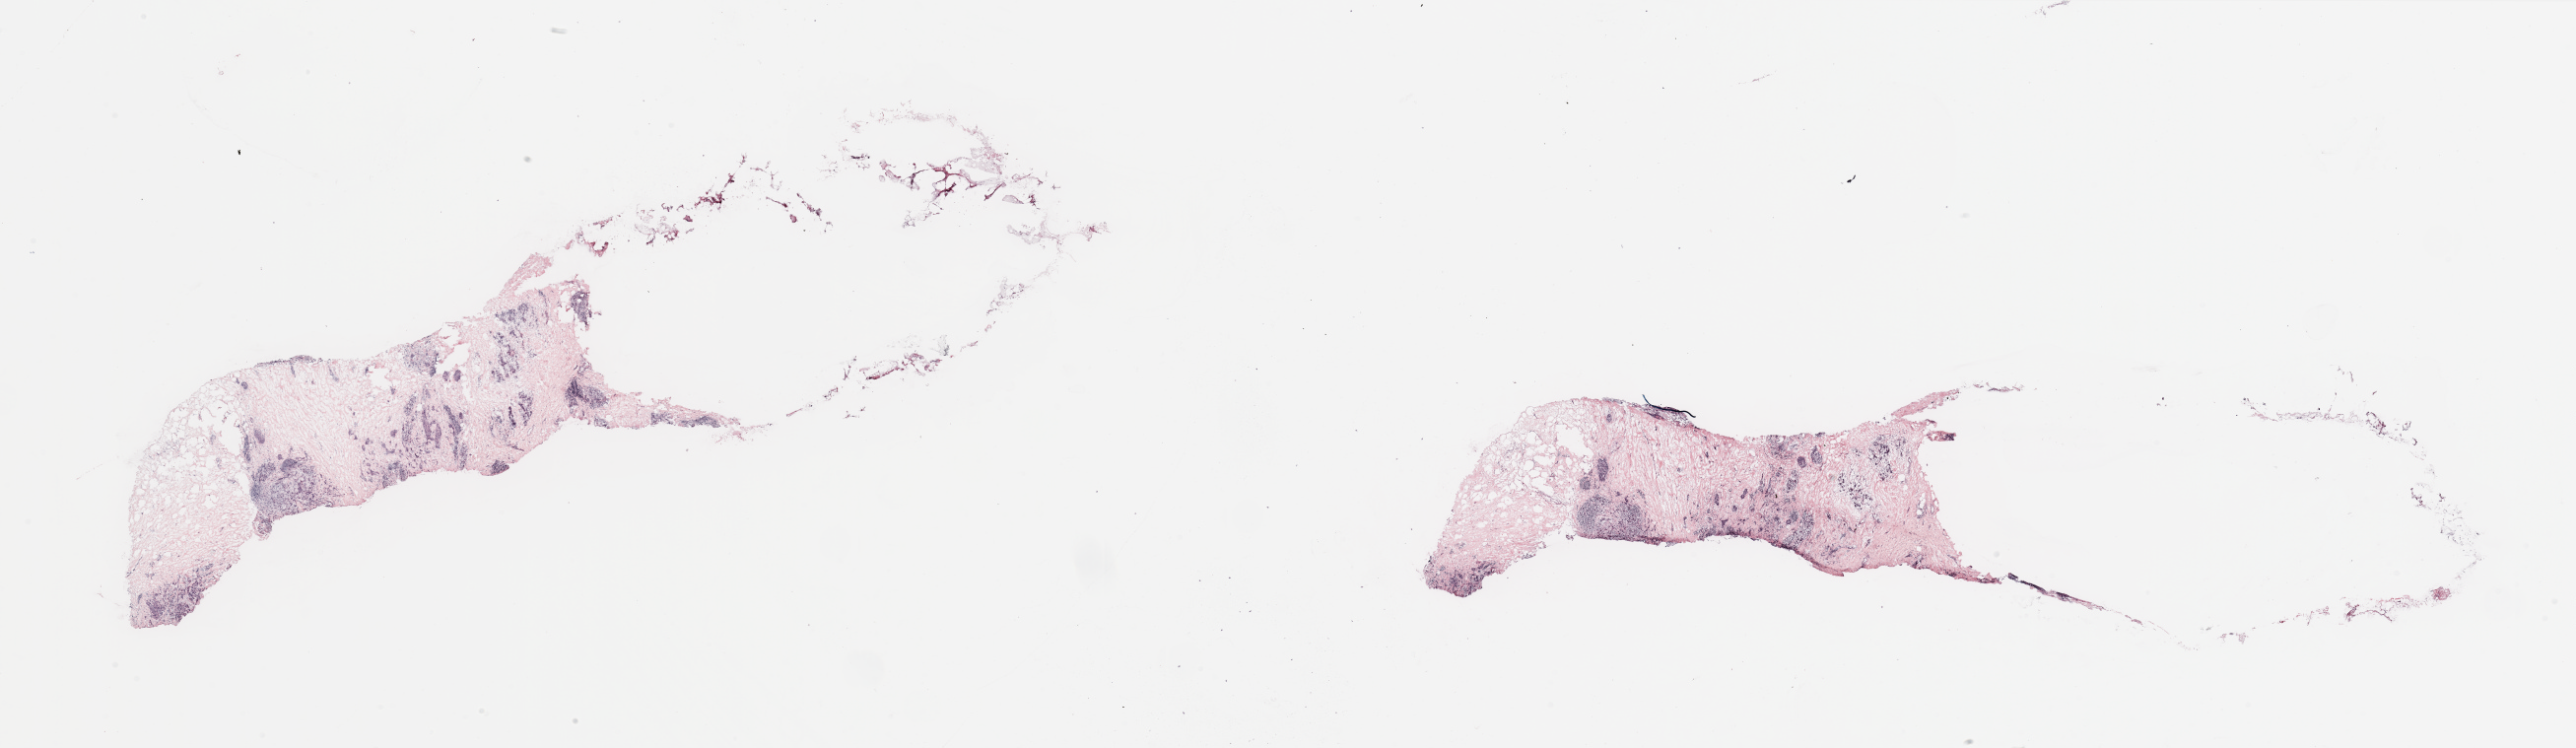
Hematoxylin and eosin (H&E) stained whole-slide image, whole scanned area (about 41.3 x 12.0 mm) shown as a low-resolution overview; breast, tumour tissue. 35-year-old female patient.
AJCC pathologic stage: IIB. Histologic diagnosis: Infiltrating duct carcinoma, NOS.